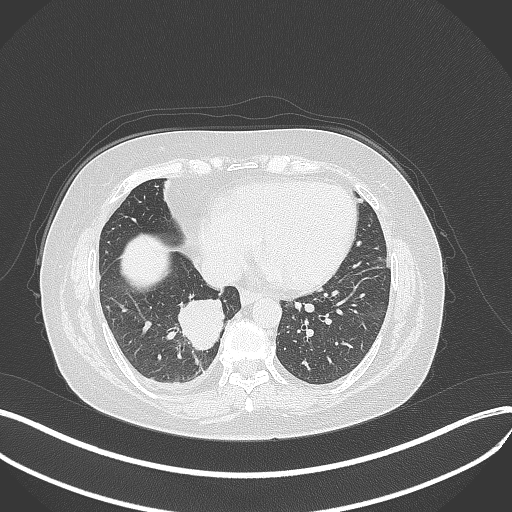
Chest CT, one axial slice. Position 123 of 381 along the scan axis. 120 kVp. Lung window (W 1500 / L -600 HU). 1 mm slice thickness. 512 × 512 image matrix, field of view 400 × 400 mm. Patient: female, 56 years. Case-level facts recorded for this patient, not image findings: clinical TNM (as recorded): T2b N1 M0.
Structures marked on this image (bounding box drawn by a radiologist):
- lung tumour (recorded histology: small cell carcinoma): bounding box <176,298,227,352> (left, top, right, bottom; pixels)